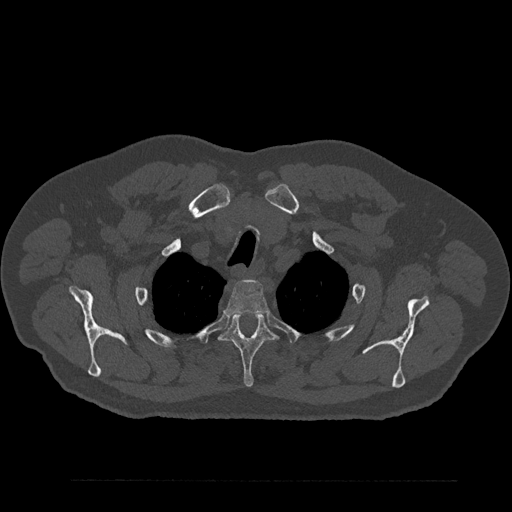
CT including the spine, one axial slice. Slice 692 of 797 in the series (ordered by position). Reconstruction kernel Br40s/3. 120 kVp. Bone window (W 1800 / L 400 HU). 0.5 mm slice thickness. 512 × 512 image matrix. Male patient, age 61 years. From the clinical record (not read from this slice): primary cancer: prostate.
Annotated regions visible in this slice (semi-automatically segmented with operator editing):
- T2 vertebra: bounding box (x1, y1, x2, y2) in pixels: (224, 279, 269, 316)
- T3 vertebra: (219, 313, 276, 387)